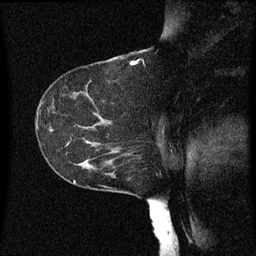
Breast MRI (dynamic contrast-enhanced), one sagittal slice; position 39 of 60 along the scan axis; dynamic contrast-enhanced series, image 2 of 3 at this slice position (ordered by acquisition); 1.5 T; TE 4.2 ms, TR 8 ms; 2 mm slice thickness; 256 × 256 image matrix, field of view 200 × 200 mm. Patient: female, 55 years.
Outlined on this slice (semi-automatically segmented with operator editing):
- analysis volume of interest (the breast-tissue region the enhancement analysis was run in; not a lesion): bounding box (x1, y1, x2, y2) in pixels: (46, 124, 149, 177)
- tumour enhancement mask (voxels above the 70 % enhancement threshold inside the analysis volume of interest): (82, 140, 129, 173)